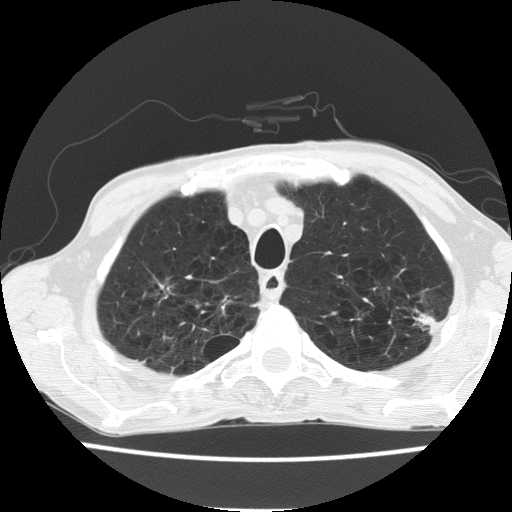
Axial slice from a low-dose chest CT screening exam. Baseline annual screen. Lung window (W 1500 / L -600 HU). Lung (sharp) reconstruction kernel (FC51). 120 kVp. Male, age 60 years at enrolment. Current smoker at enrolment.
Expert-annotated lung lesion, bounding box <396,291,455,349> (left, top, right, bottom; pixels). Screening reader's record for this exam: no non-calcified nodule ≥4 mm recorded. Participant outcome: lung cancer diagnosed 490 days after this screen — bronchiolo-alveolar carcinoma, mucinous, left upper lobe, stage IV (AJCC 6th edition).